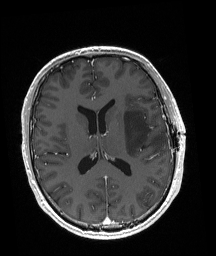
Brain MRI from a brain-tumour surgery series, one axial slice; slice 87 of 192 in the series (ordered by position); T1-weighted post-contrast; 1 mm slice thickness; 216 × 256 image matrix. From the clinical record (not read from this slice): histopathology: Astrocytoma; WHO grade: 3; IDH mutation: yes; tumour location: Left Posterior Frontal.
Structures marked on this image (expert manual segmentation):
- tumour: box from (x=123, y=110) to (x=165, y=157) px